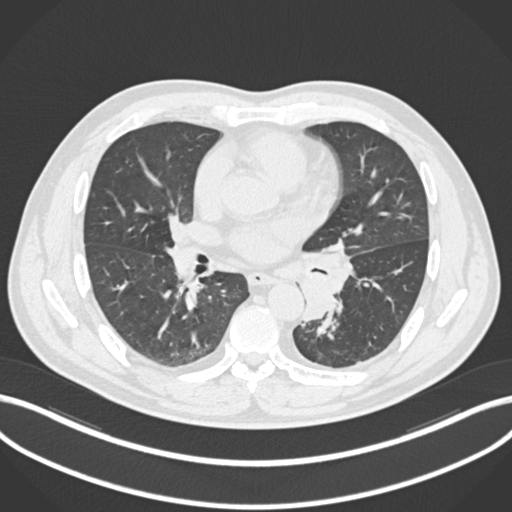
Chest CT, one axial slice. Slice 114 of 223 in the series (ordered by position). Lung window (W 1500 / L -600 HU). 1 mm slice thickness. 512 × 512 image matrix, field of view 400 × 400 mm. Male patient, age 50 years. Case-level facts recorded for this patient, not image findings: clinical TNM (as recorded): T2a N3 M0.
Annotated regions visible in this slice (rectangle marked by the reading radiologist):
- lung tumour (recorded histology: squamous cell carcinoma): bounding box <294,237,351,323> (left, top, right, bottom; pixels)